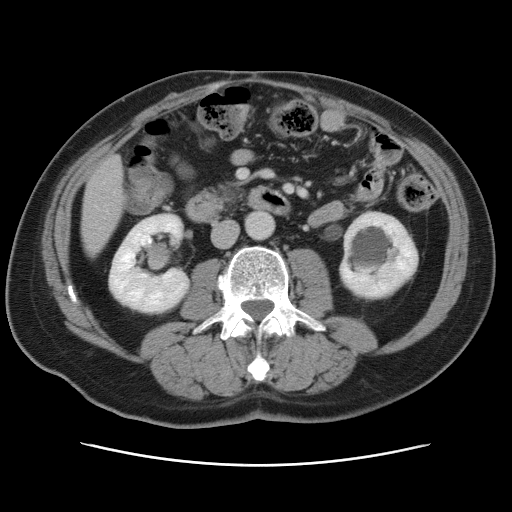
Contrast-enhanced abdominal CT, one axial slice; position 18 of 80 along the scan axis; intravenous contrast given; soft-tissue window (W 400 / L 40 HU); 5 mm slice thickness; 512 × 512 image matrix. Male patient, age 69 years. From the clinical record (not read from this slice): diagnosis: colorectal cancer liver metastases, imaged before liver resection; multiple liver metastases: no; largest metastasis: 5 cm; disease in both lobes: yes.
Annotated regions visible in this slice (outlined manually by an expert reader):
- liver: box from (x=82, y=157) to (x=124, y=253) px
- planned liver remnant (the part of the liver to remain after resection): (x=82, y=225)–(x=112, y=254)